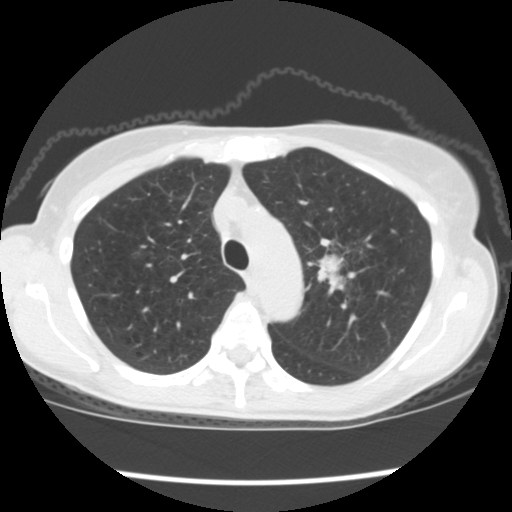
Low-dose screening chest CT, axial slice. Baseline annual screen. Lung window (W 1500 / L -600 HU). Slice 41 of 176 in the series. 512 × 512 image matrix, field of view 318 × 318 mm. Female participant, aged 67 years at enrolment. Former smoker at enrolment.
Expert-annotated lung lesion, bounding box [x1, y1, x2, y2] px = [307, 234, 381, 311]. Reader record for this screening exam (exam-level; its link to the box is not recorded): non-calcified nodule or mass ≥4 mm, left upper lobe, 34 × 32 mm, spiculated (stellate) margins, soft tissue attenuation, pre-existing on the prior screen: no. Participant outcome: lung cancer diagnosed 17 days after this screen — small cell carcinoma, NOS, left upper lobe, stage IIIA (AJCC 6th edition), 40 mm at pathology.